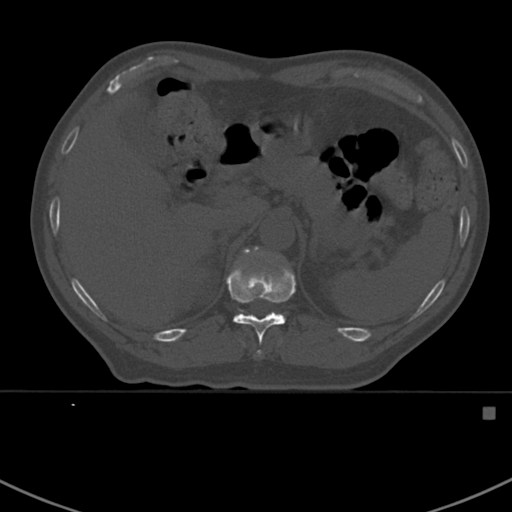
CT including the spine, one axial slice; slice 345 of 412 in the series (ordered by position); reconstruction kernel Br40s; 120 kVp; bone window (W 1800 / L 400 HU); 512 × 512 image matrix. Male patient, age 59 years. Case-level facts recorded for this patient, not image findings: primary cancer: prostate.
Annotated regions visible in this slice (semi-automatically segmented with operator editing):
- T11 vertebra: bounding box <226,252,296,357> (left, top, right, bottom; pixels)
- T12 vertebra: <238,247,278,313>